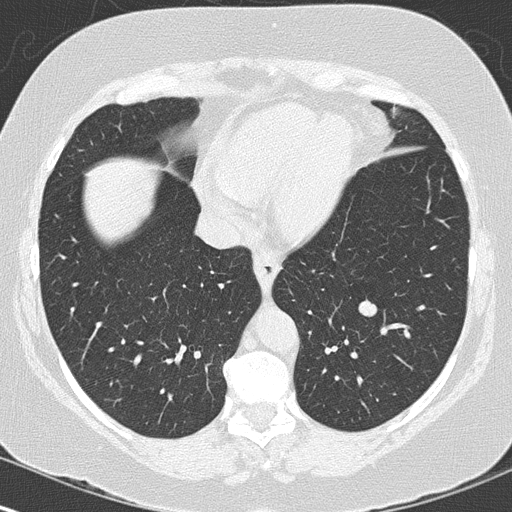
Low-dose screening chest CT, one axial slice; slice 47 of 144 in the series (ordered by position); reconstruction kernel B50f; lung window (W 1500 / L -600 HU); 512 × 512 image matrix.
Outlined on this slice (outlined manually by an expert reader):
- lesion 1 (tumor, lower lobe of left lung): bounding box <358,299,377,317> (left, top, right, bottom; pixels)